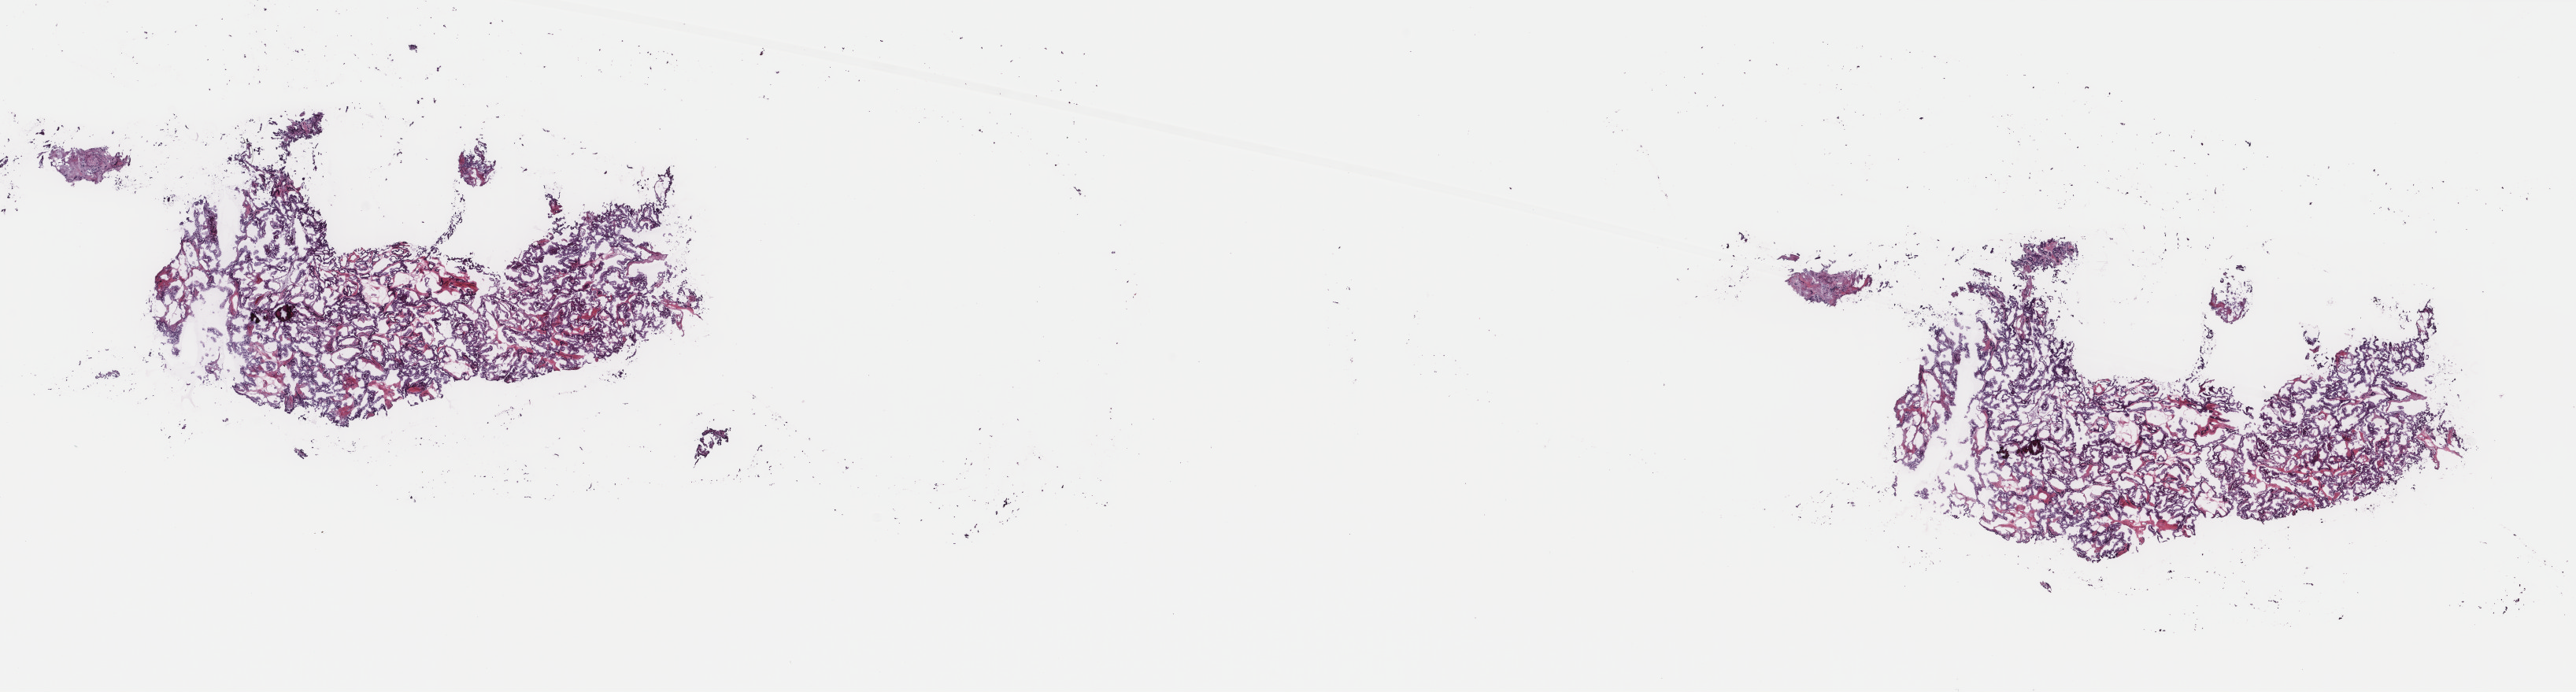
Digitized Hematoxylin and eosin (H&E) stained tissue section (whole slide), low-resolution overview of the scanned area, about 26.0 x 7.0 mm, frozen section from the top of the tissue portion, thyroid, primary tumour sample. Female, age 41 years at initial diagnosis. Pathologist review of this section (percent, as recorded): tumour cells 80%, tumour nuclei 100%, normal cells 0%, stromal cells 20%, necrosis 0%. Inflammatory infiltration, as recorded: lymphocyte infiltration 2%, monocyte infiltration 0%, neutrophil infiltration 0%.
Diagnosis: Papillary adenocarcinoma, NOS. AJCC pathologic stage: I (6th edition). Laterality: right.